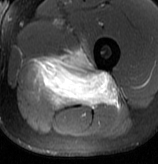
MRI of an extremity soft-tissue mass, one axial slice. Slice 50 of 70 in the series (ordered by position). T2-weighted fat-saturated. MR volume resampled by the dataset authors to the PET/CT grid (not the native acquisition matrix). 158 × 164 image matrix. Male patient. Case-level facts recorded for this patient, not image findings: histological type: extraskeletal osteosarcoma; grade: high; site of the primary tumour: left adductur.
Structures marked on this image (expert contour drawn on MRI and transferred to this co-registered scan by the dataset authors):
- gross tumour volume (mass): bounding box [x1, y1, x2, y2] px = [31, 48, 119, 108]